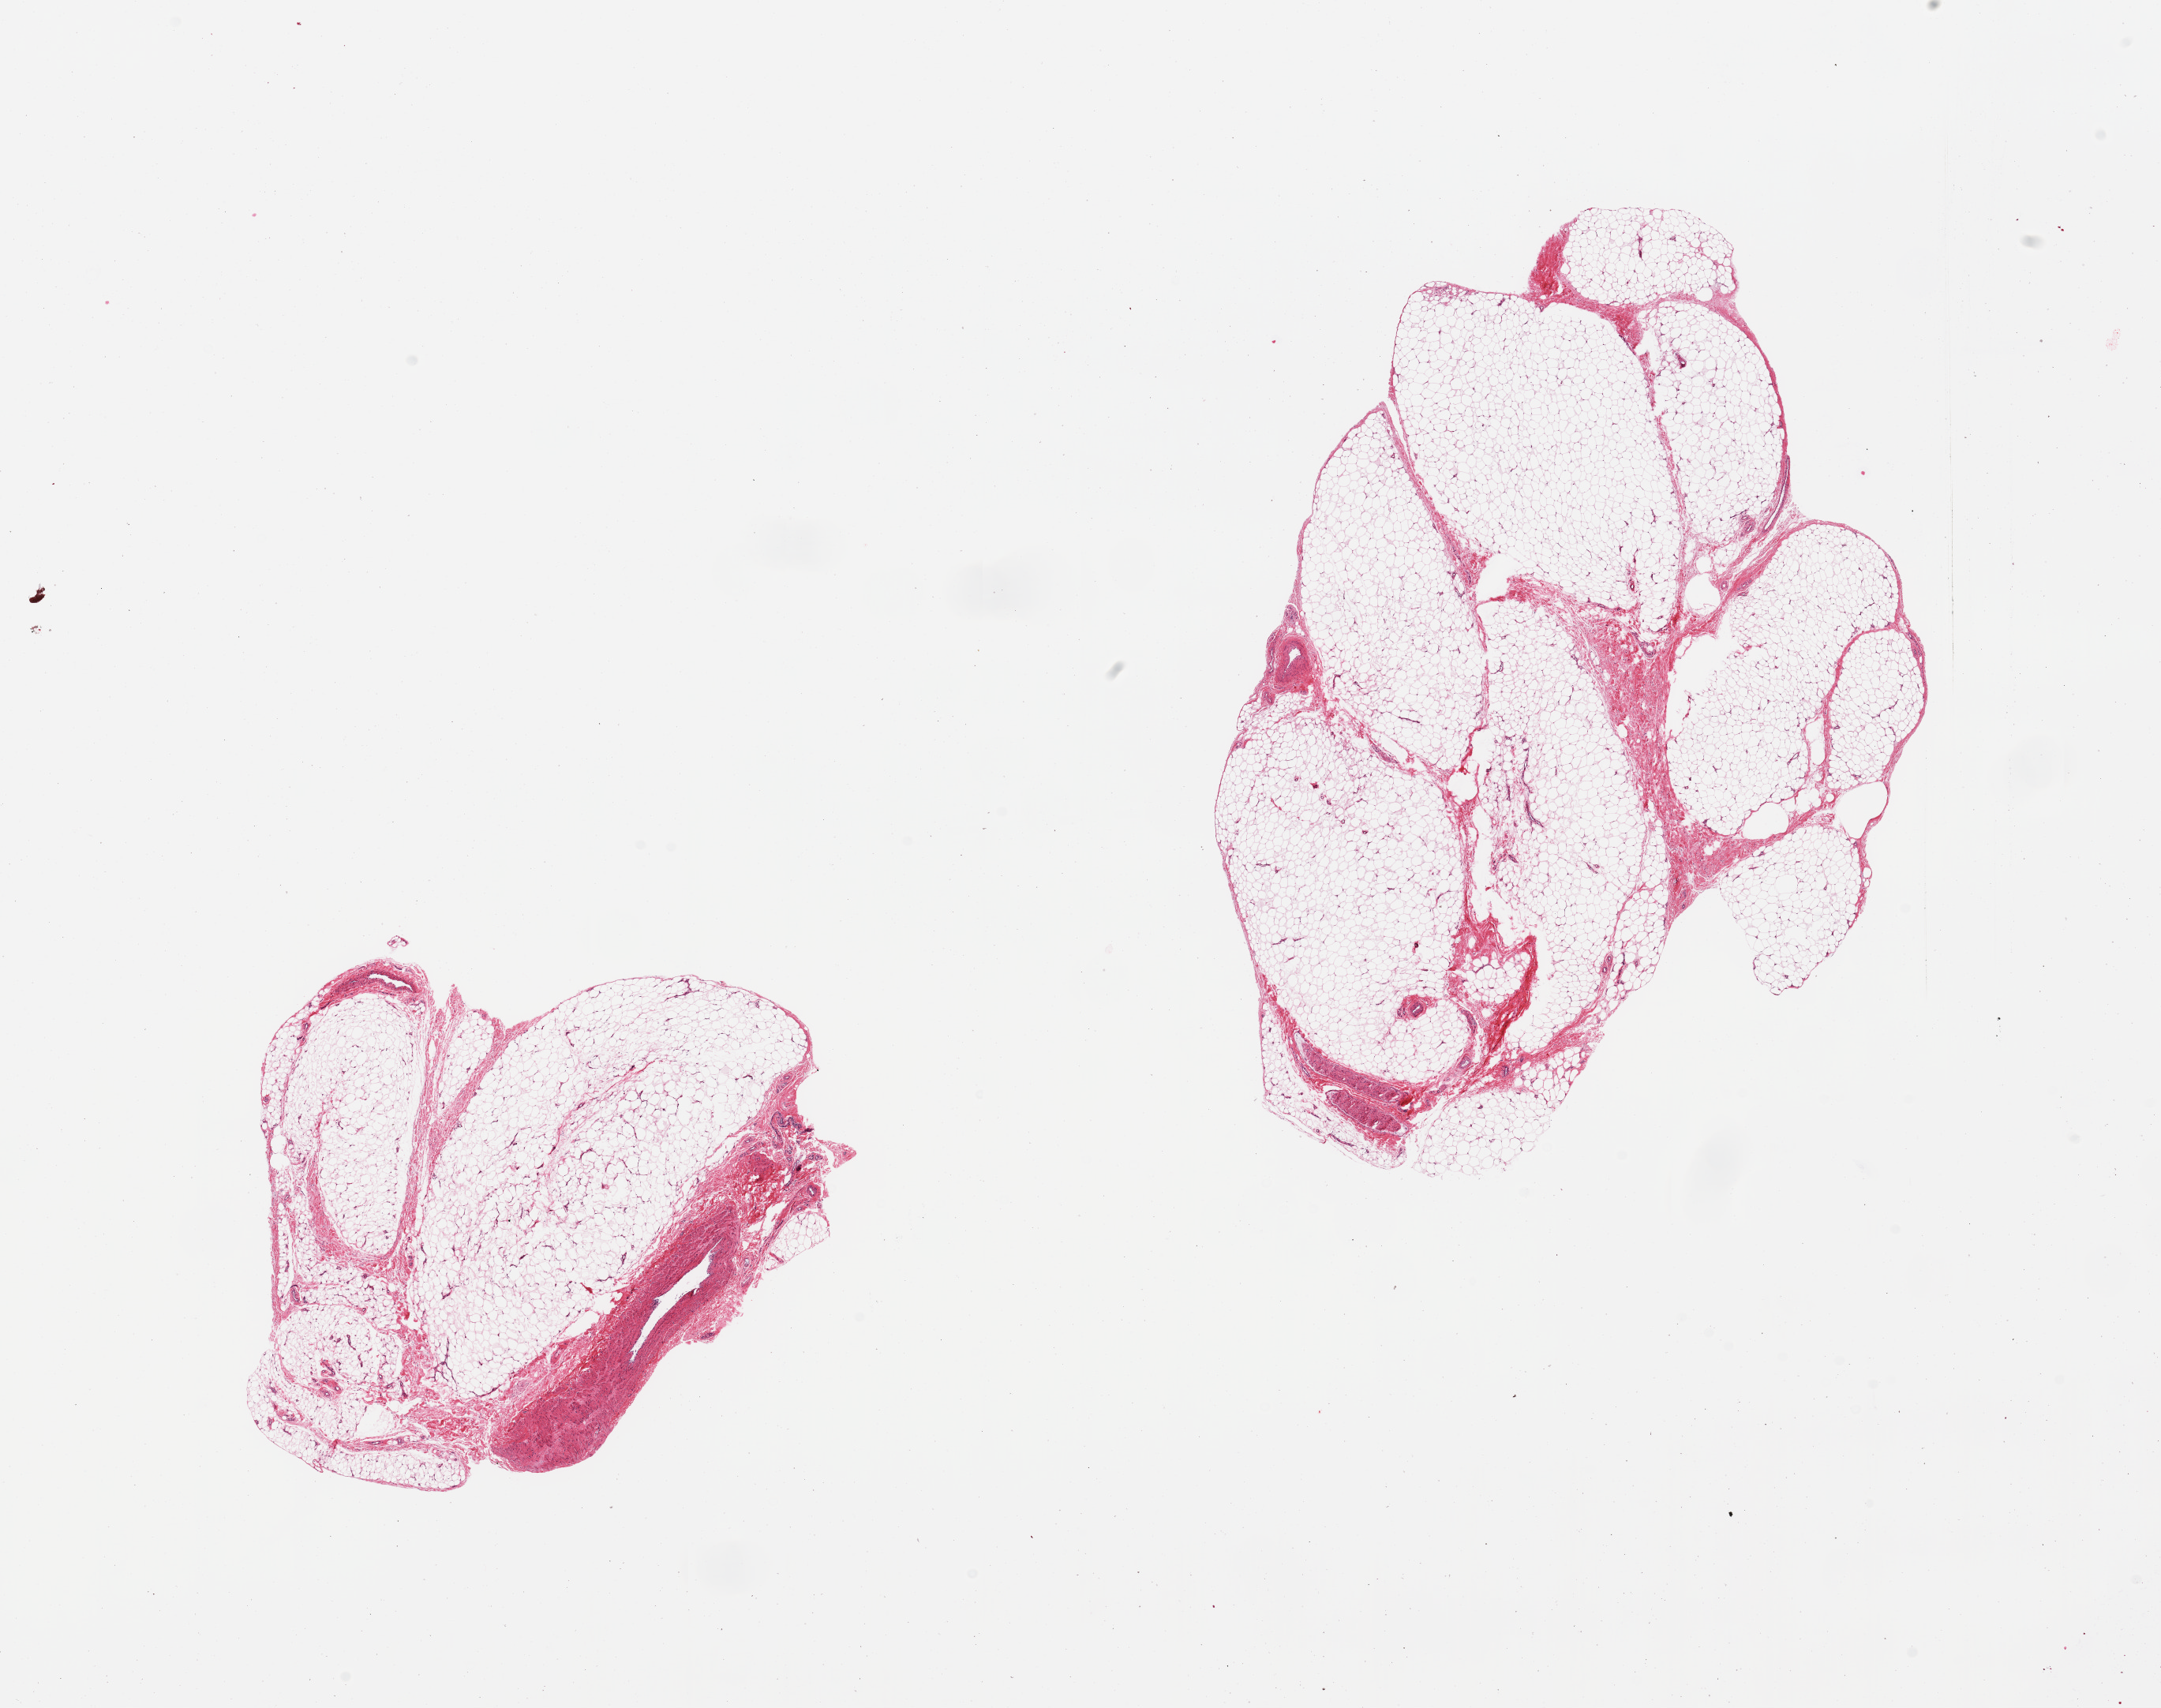
Whole-slide image, hematoxylin and eosin (H&E) stain, brightfield, a low-resolution overview of the entire scanned area, about 21.7 x 17.1 mm (slide scanned at 20x); PAXgene-fixed paraffin-embedded (PFPE) section; sampled site (target tissue): adipose tissue; donor tissue sample. Female donor.
• review note (as recorded): 2 pieces; mature adipose tissue, ~10% is vessels/nerve/connective tissue